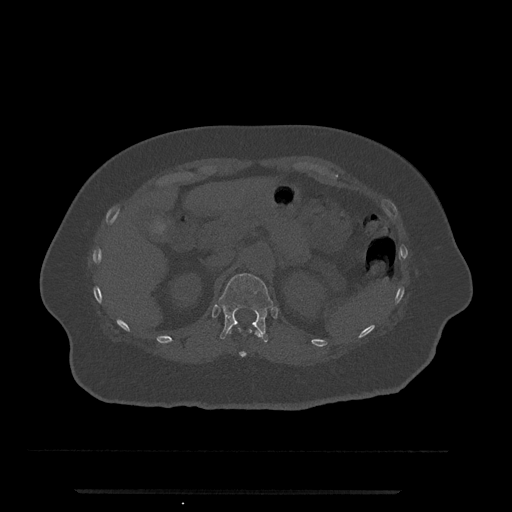
CT including the spine, one axial slice; position 186 of 797 along the scan axis; reconstruction kernel Br40s/3; 120 kVp; bone window (W 1800 / L 400 HU); 0.5 mm slice thickness; 512 × 512 image matrix, field of view 440 × 440 mm. Patient: female, 51 years. From the clinical record (not read from this slice): primary cancer: neuro; vertebrae with lytic lesions (as recorded): T8.
Annotated regions visible in this slice (semi-automatically segmented with operator editing):
- T11 vertebra: box from (x=229, y=327) to (x=261, y=357) px
- T12 vertebra: (x=218, y=273)–(x=273, y=342)